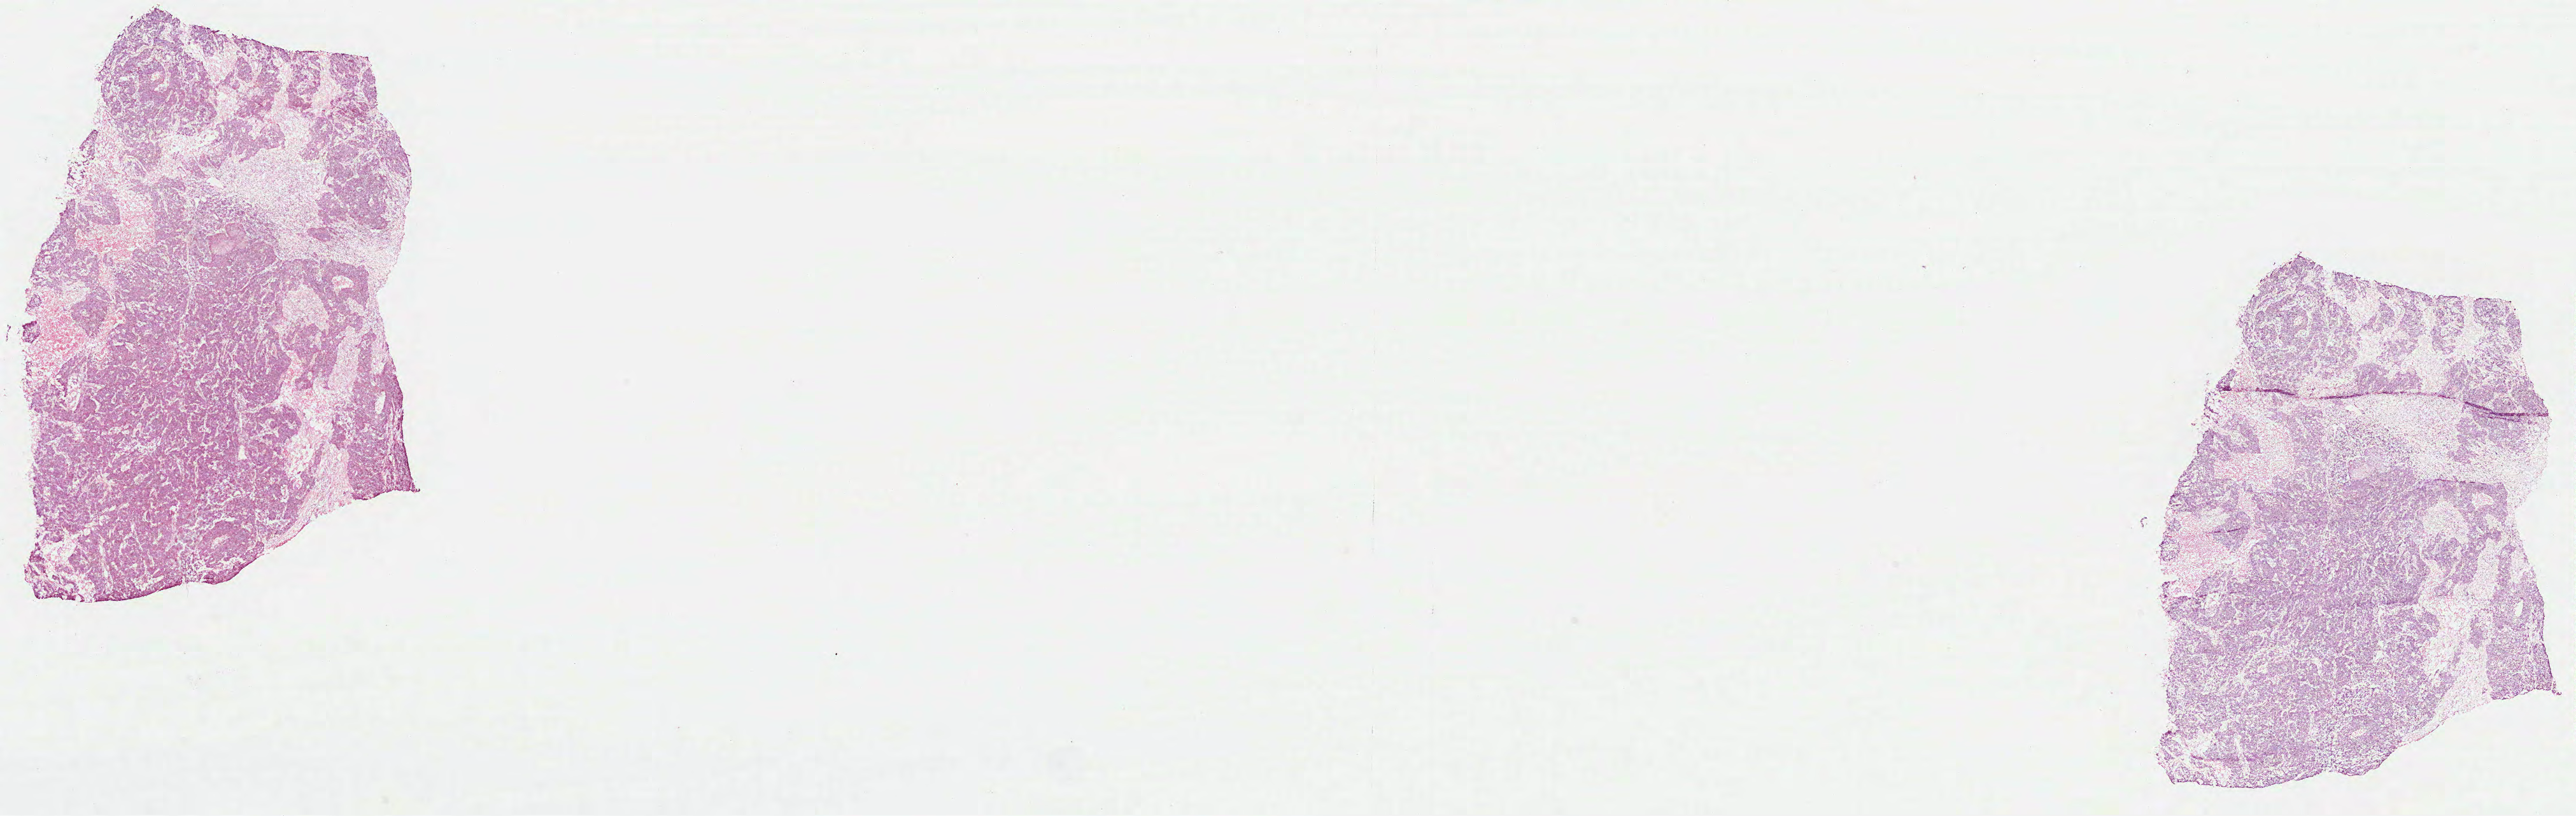
Digitized Hematoxylin and eosin (H&E) stained tissue section (whole slide), whole scanned area (about 32.6 x 10.3 mm) shown as a low-resolution overview. Formalin-fixed paraffin-embedded (FFPE) diagnostic section. Head and neck, primary tumour sample. Patient: male, age at initial diagnosis 48 years. Histologic grade: G3 (poorly differentiated).
Laterality: left. Pathologic diagnosis: Squamous cell carcinoma, NOS (tonsil, NOS). AJCC pathologic stage: IVA (7th edition). TNM: T2 N2b M0.